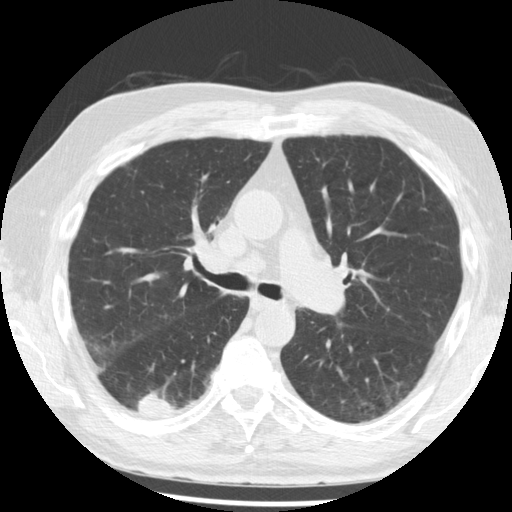
Low-dose screening chest CT, one axial slice. Slice 130 of 221 in the series (ordered by position). Lung window (W 1500 / L -600 HU). 2.5 mm slice thickness. 512 × 512 image matrix, field of view 350 × 350 mm.
Annotated regions visible in this slice (outlined manually by an expert reader):
- lesion 1 (tumor, lower lobe of right lung): box from (x=138, y=392) to (x=178, y=415) px